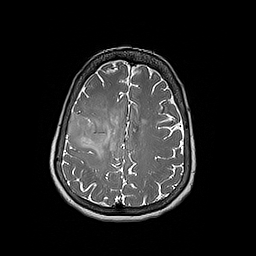
Brain MRI from a brain-tumour surgery series, one axial slice. Position 69 of 192 along the scan axis. 1 mm slice thickness. 256 × 256 image matrix, field of view 250 × 250 mm. From the clinical record (not read from this slice): histopathology: Oligodendroglioma; WHO grade: 3; IDH mutation: yes; tumour location: Right Frontal.
Structures marked on this image (expert manual segmentation):
- tumour: bounding box (x1, y1, x2, y2) in pixels: (66, 112, 110, 148)